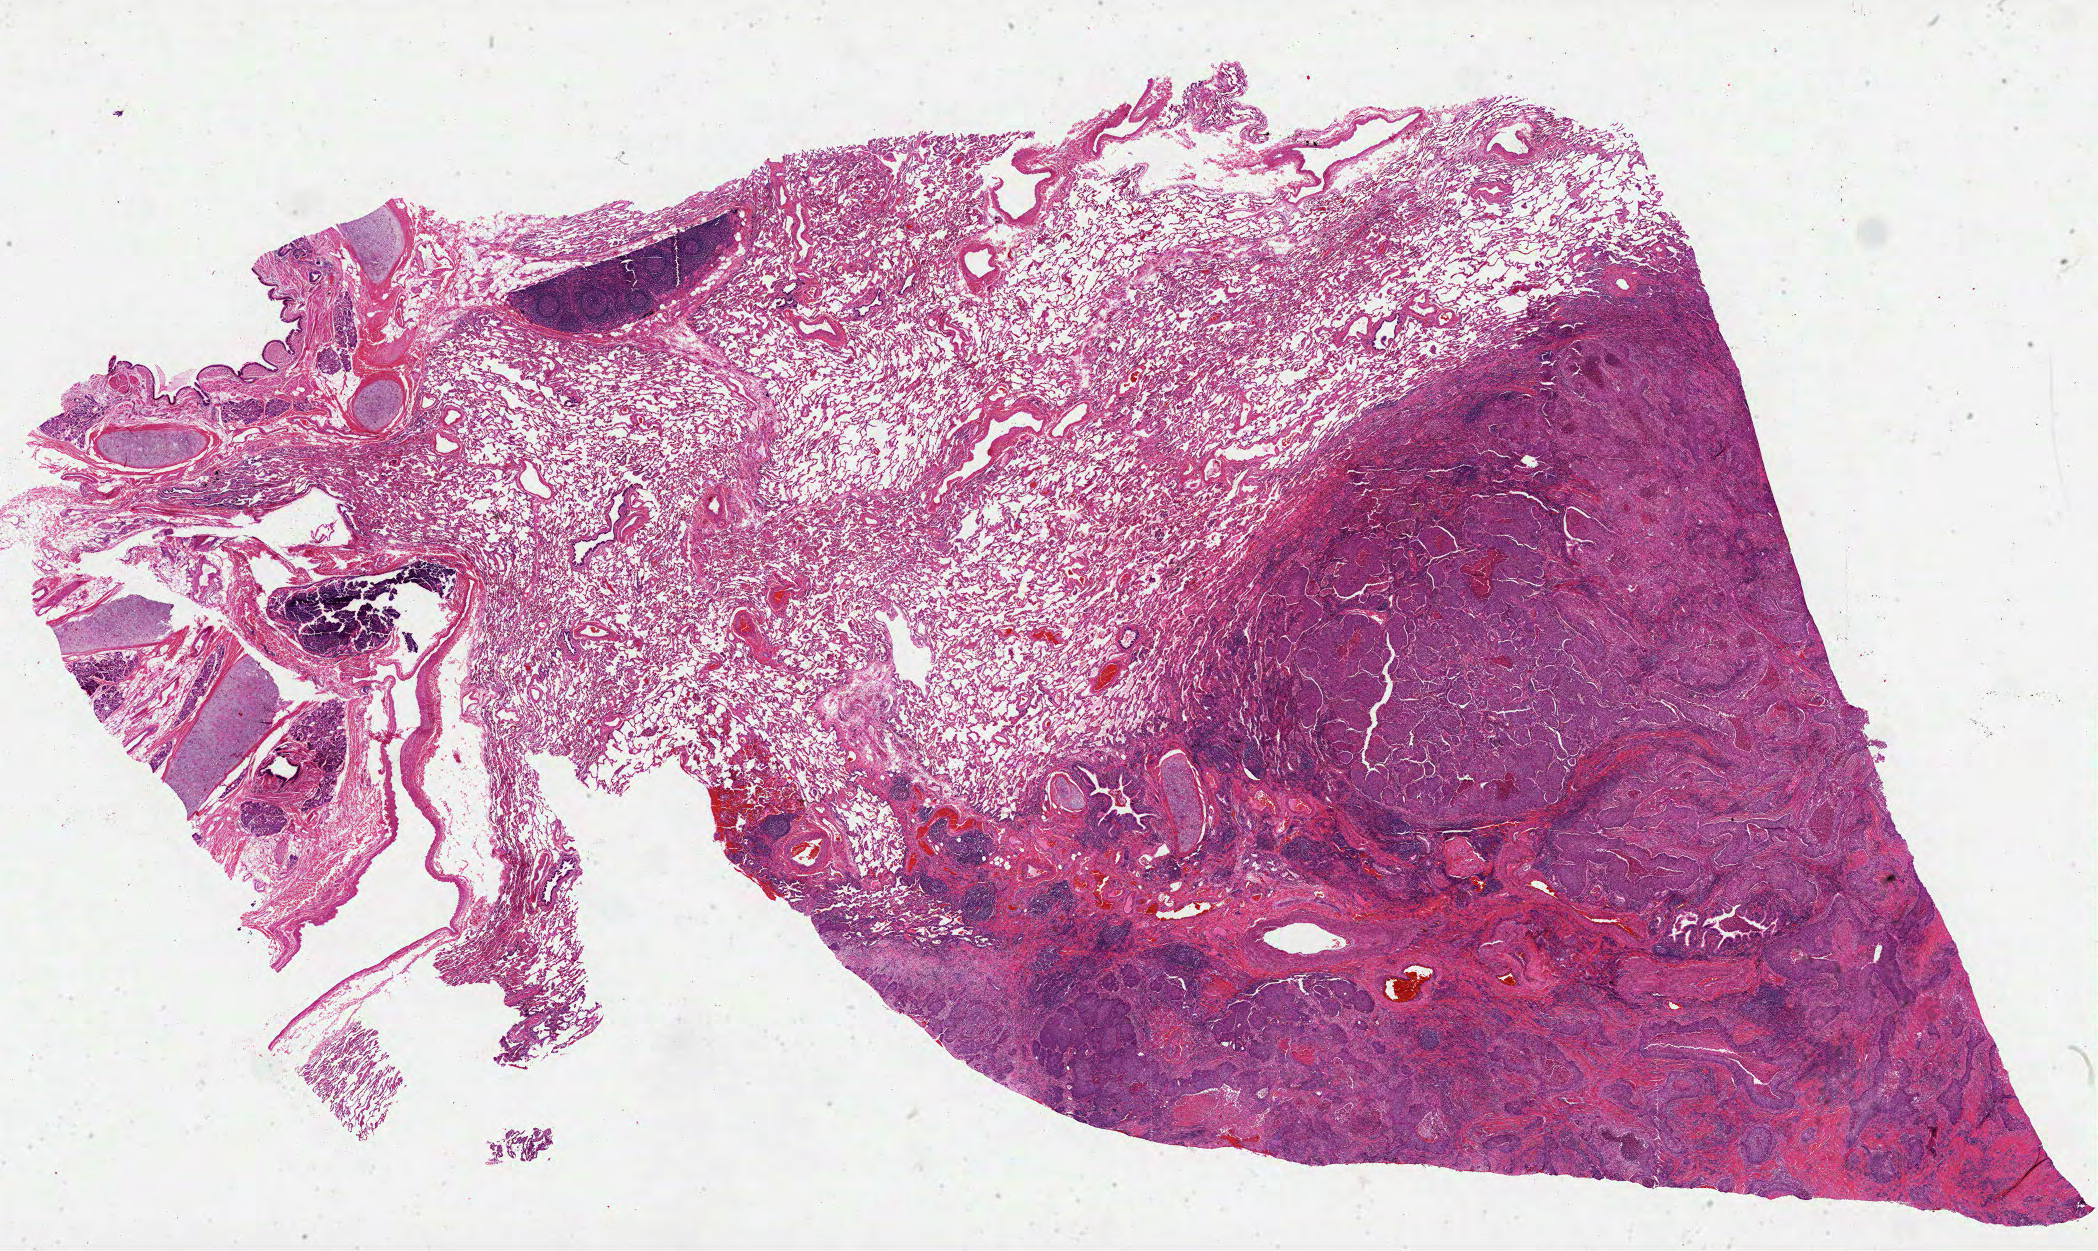
H&E-stained whole-slide image — a low-resolution overview of the entire scanned area, about 33.8 x 20.2 mm (acquisition: 40x scan). Formalin-fixed paraffin-embedded (FFPE) diagnostic section. Sample: primary tumour, lung. Male, age 68 years at initial diagnosis.
Histologic diagnosis: Squamous cell carcinoma, NOS (upper lobe, lung). AJCC pathologic stage: IB.